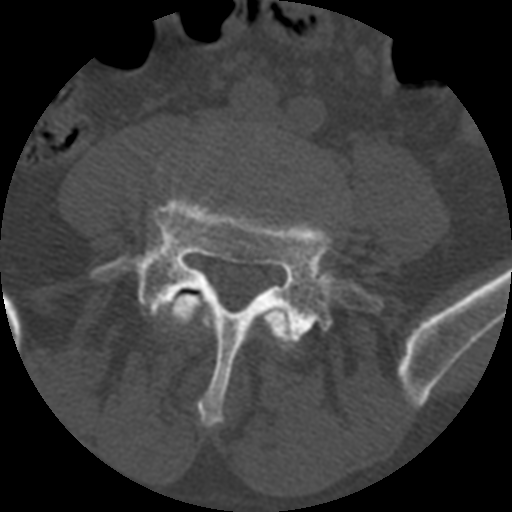
CT including the spine, one axial slice; slice 263 of 399 in the series (ordered by position); reconstruction kernel STANDARD; bone window (W 1800 / L 400 HU); 1.25 mm slice thickness; 512 × 512 image matrix, field of view 160 × 160 mm. Patient age 71 years. Case-level facts recorded for this patient, not image findings: primary cancer: prostate.
Structures marked on this image (semi-automatically segmented with operator editing):
- L4 vertebra: bounding box (x1, y1, x2, y2) in pixels: (167, 293, 294, 346)
- L5 vertebra: (91, 194, 383, 426)